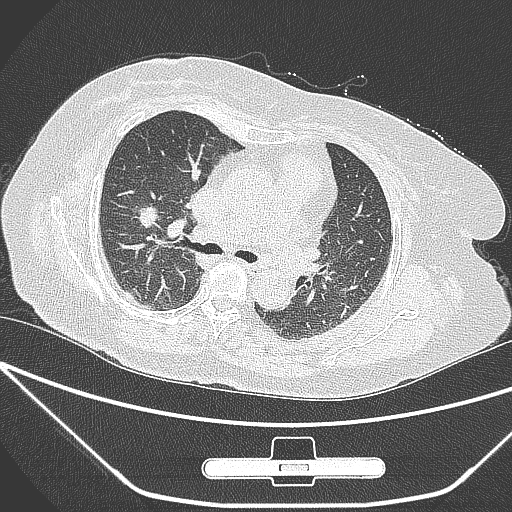
Chest CT, one axial slice. Position 164 of 245 along the scan axis. Lung window (W 1500 / L -600 HU). 512 × 512 image matrix, field of view 365 × 365 mm. Patient: female, 65 years. From the clinical record (not read from this slice): clinical TNM (as recorded): T1c N0 M0.
Outlined on this slice (rectangle marked by the reading radiologist):
- lung tumour (recorded histology: adenocarcinoma): bounding box (x1, y1, x2, y2) in pixels: (132, 195, 167, 237)